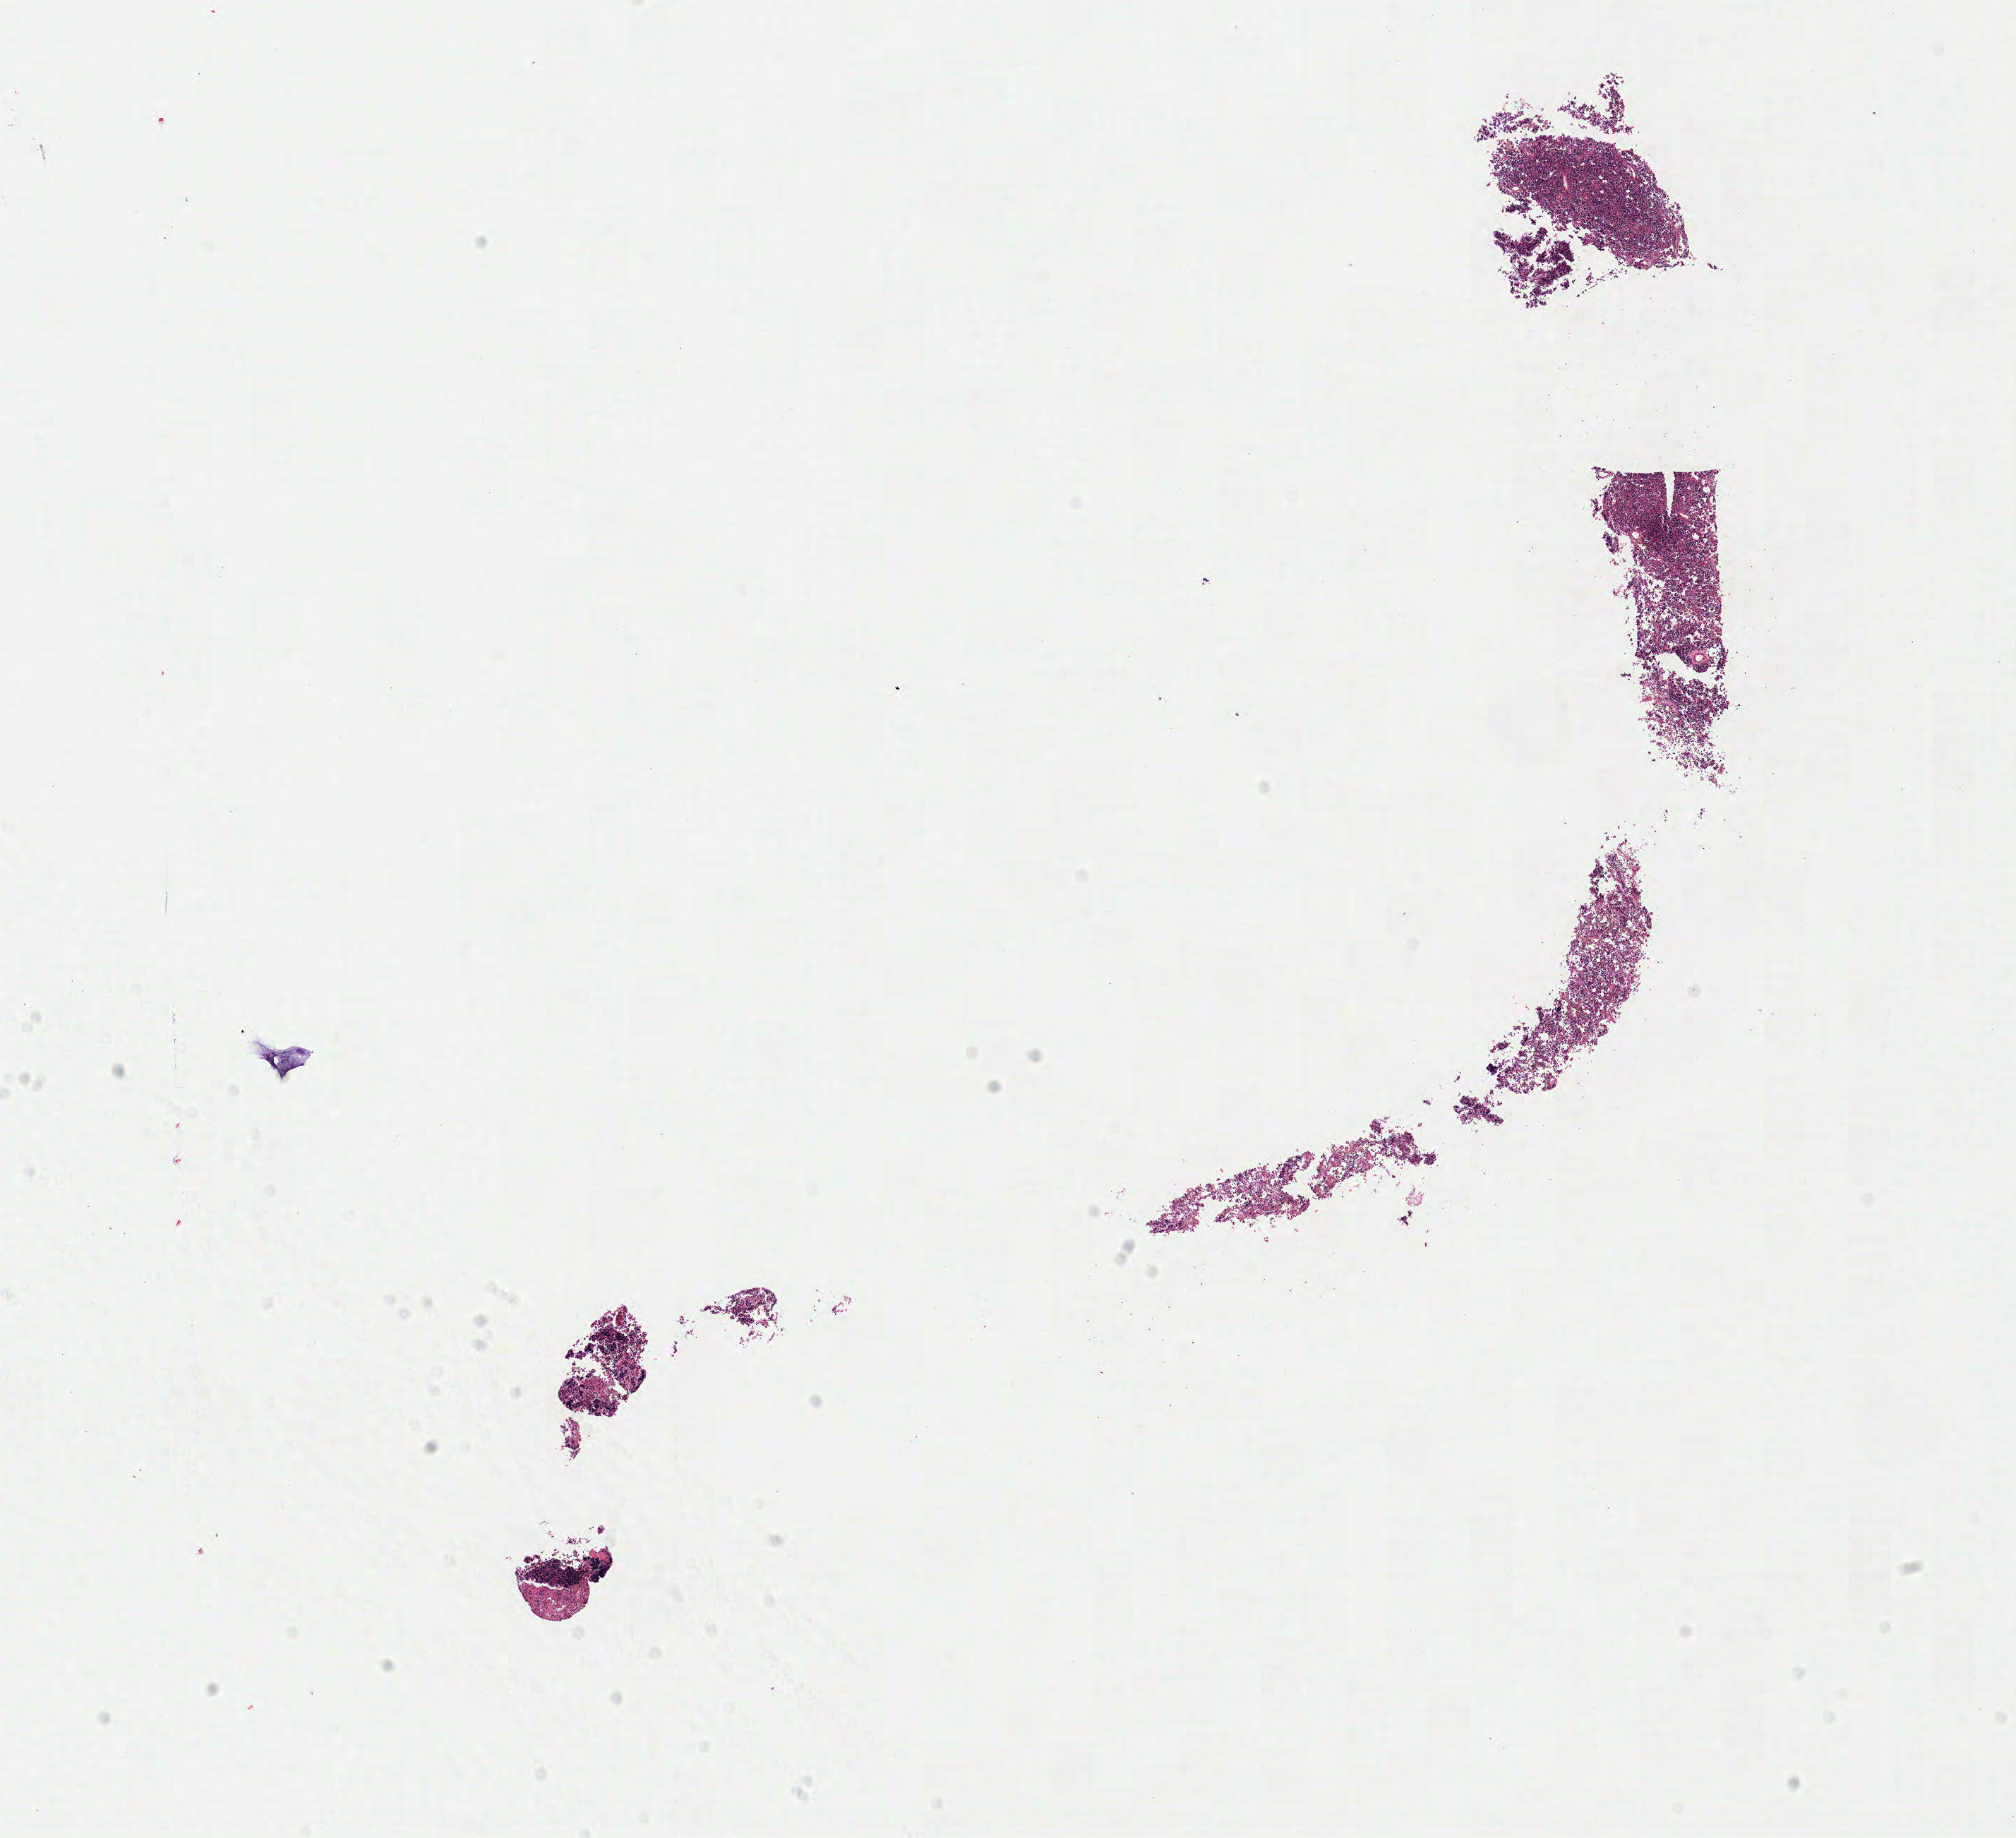
Whole-slide image, hematoxylin and eosin (H&E) stain, low-resolution overview of the scanned area, about 11.3 x 10.3 mm. Specimen: tumor tissue. Anatomic site: ovary. Female, age 7 years at initial diagnosis.
Diagnosis: Burkitt lymphoma, NOS.